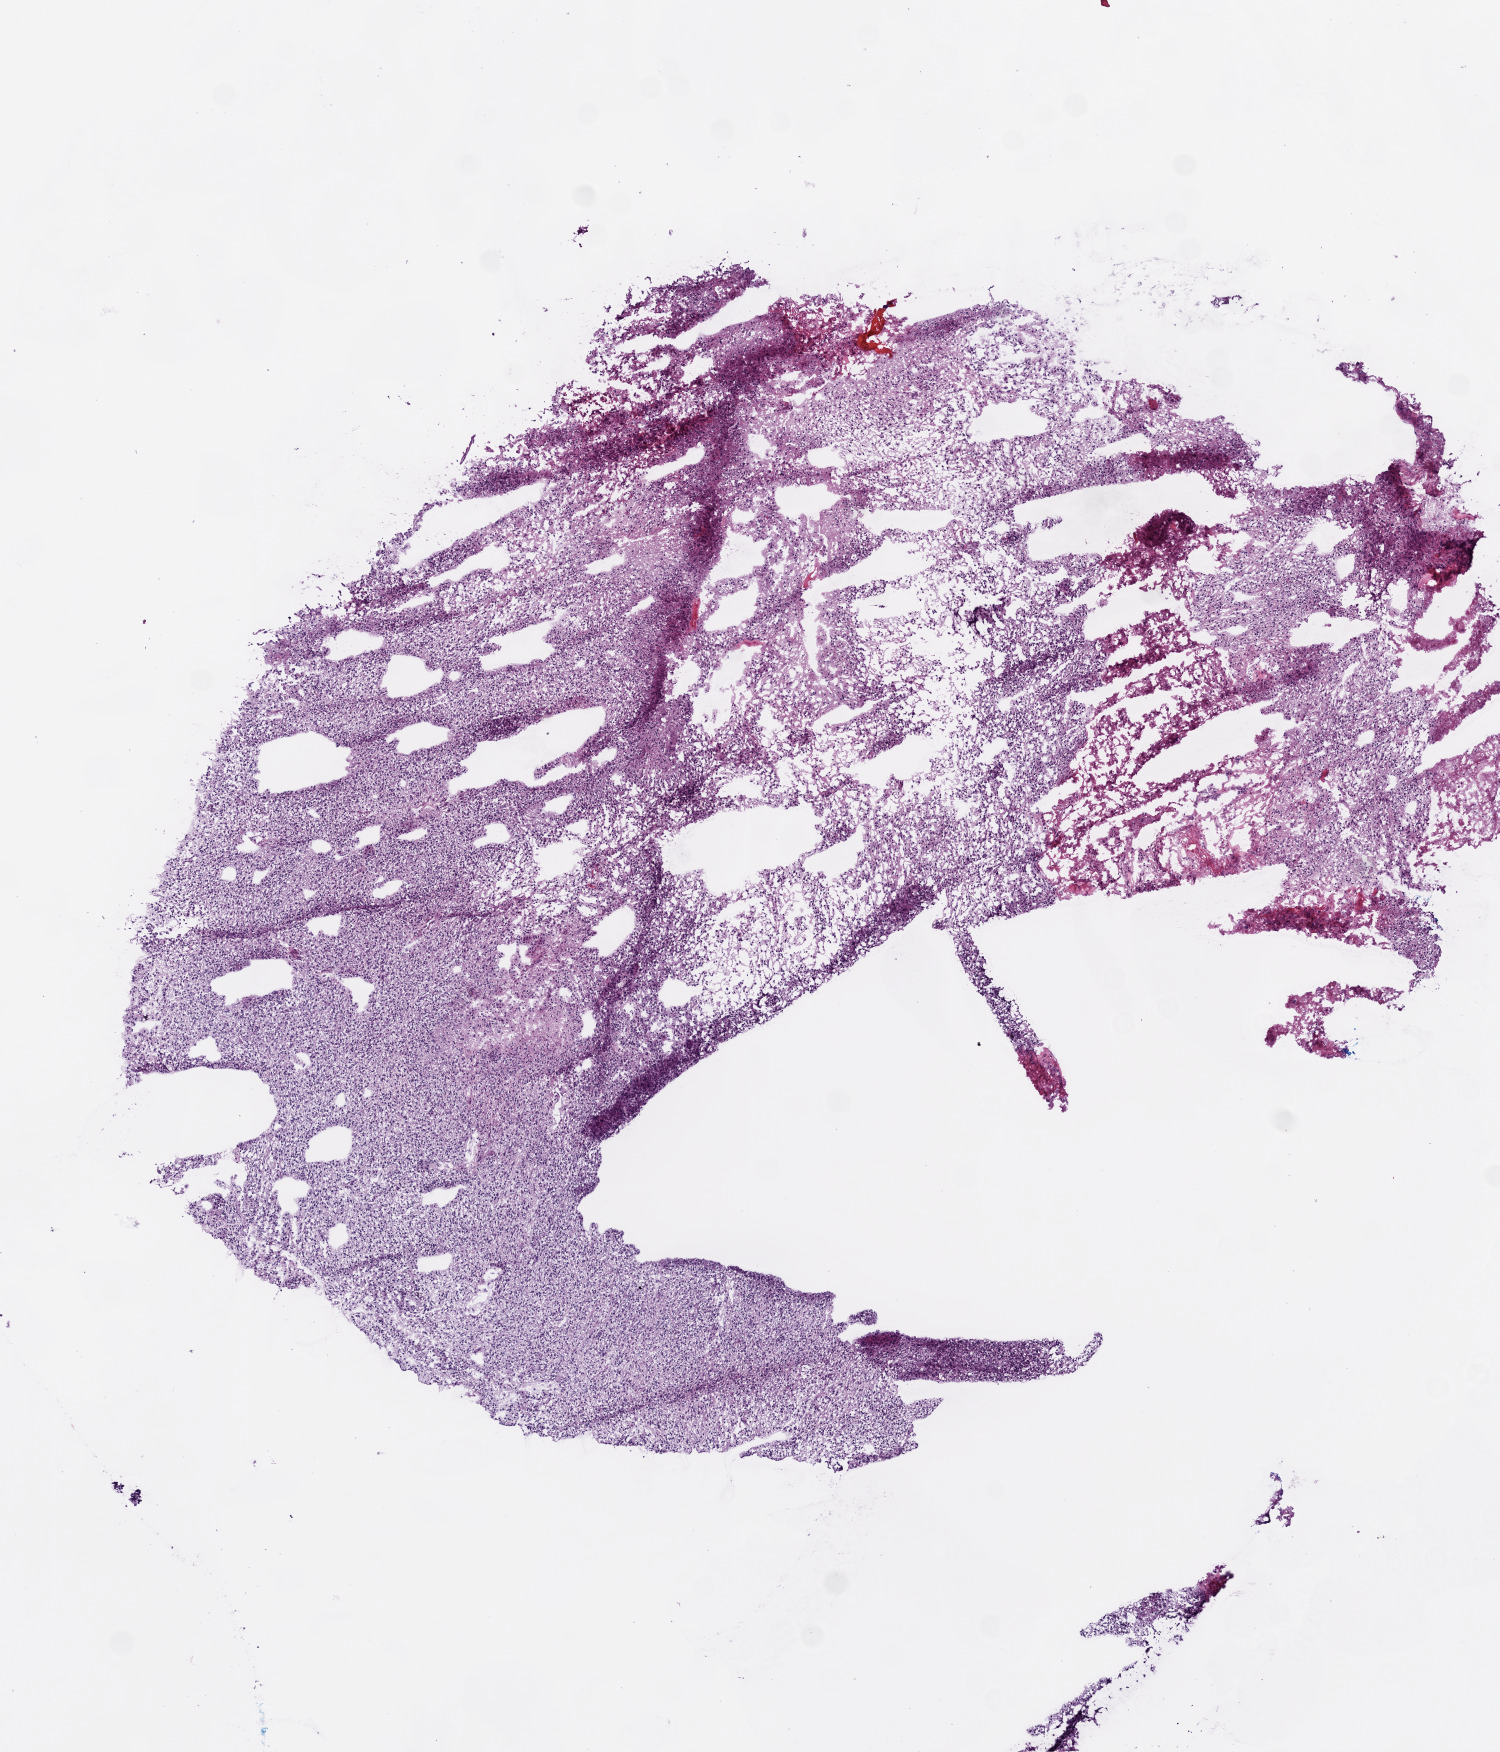
Whole-slide histology image, H&E-stained, low-resolution overview of the scanned area, about 6.0 x 7.0 mm, frozen section from the bottom of the tissue portion, sample: primary tumour, brain. Patient: male, age at initial diagnosis 83 years. Slide review estimates, as recorded: tumour cells 95%, tumour nuclei 85%, normal cells 0%, stromal cells 0%, necrosis 5%.
* histologic diagnosis: Glioblastoma